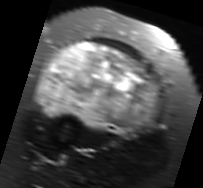
MRI of an extremity soft-tissue mass, one axial slice; position 39 of 91 along the scan axis; T2-weighted fat-saturated; MR volume resampled by the dataset authors to the PET/CT grid (not the native acquisition matrix); 203 × 188 image matrix. Female patient. From the clinical record (not read from this slice): histological type: malignant solitary fibrous tumor; grade: intermediate; site of the primary tumour: right thigh.
Annotated regions visible in this slice (expert contour drawn on MRI and transferred to this co-registered scan by the dataset authors):
- gross tumour volume including surrounding oedema: bounding box <35,40,162,137> (left, top, right, bottom; pixels)
- gross tumour volume (mass): <40,40,157,134>